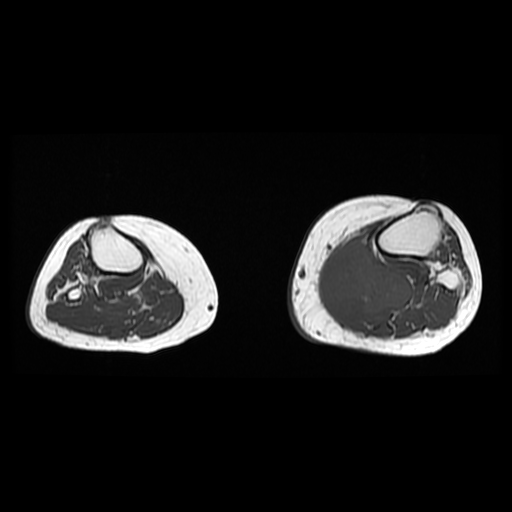
MRI of an extremity soft-tissue mass, one axial slice. 6 mm slice thickness. 512 × 512 image matrix, field of view 330 × 330 mm. Female patient. From the clinical record (not read from this slice): histological type: extraskeletal high grade osteogenic sarcoma; grade: high; site of the primary tumour: left calf.
Outlined on this slice (expert manual segmentation):
- gross tumour volume (mass): bounding box [x1, y1, x2, y2] px = [316, 238, 414, 323]